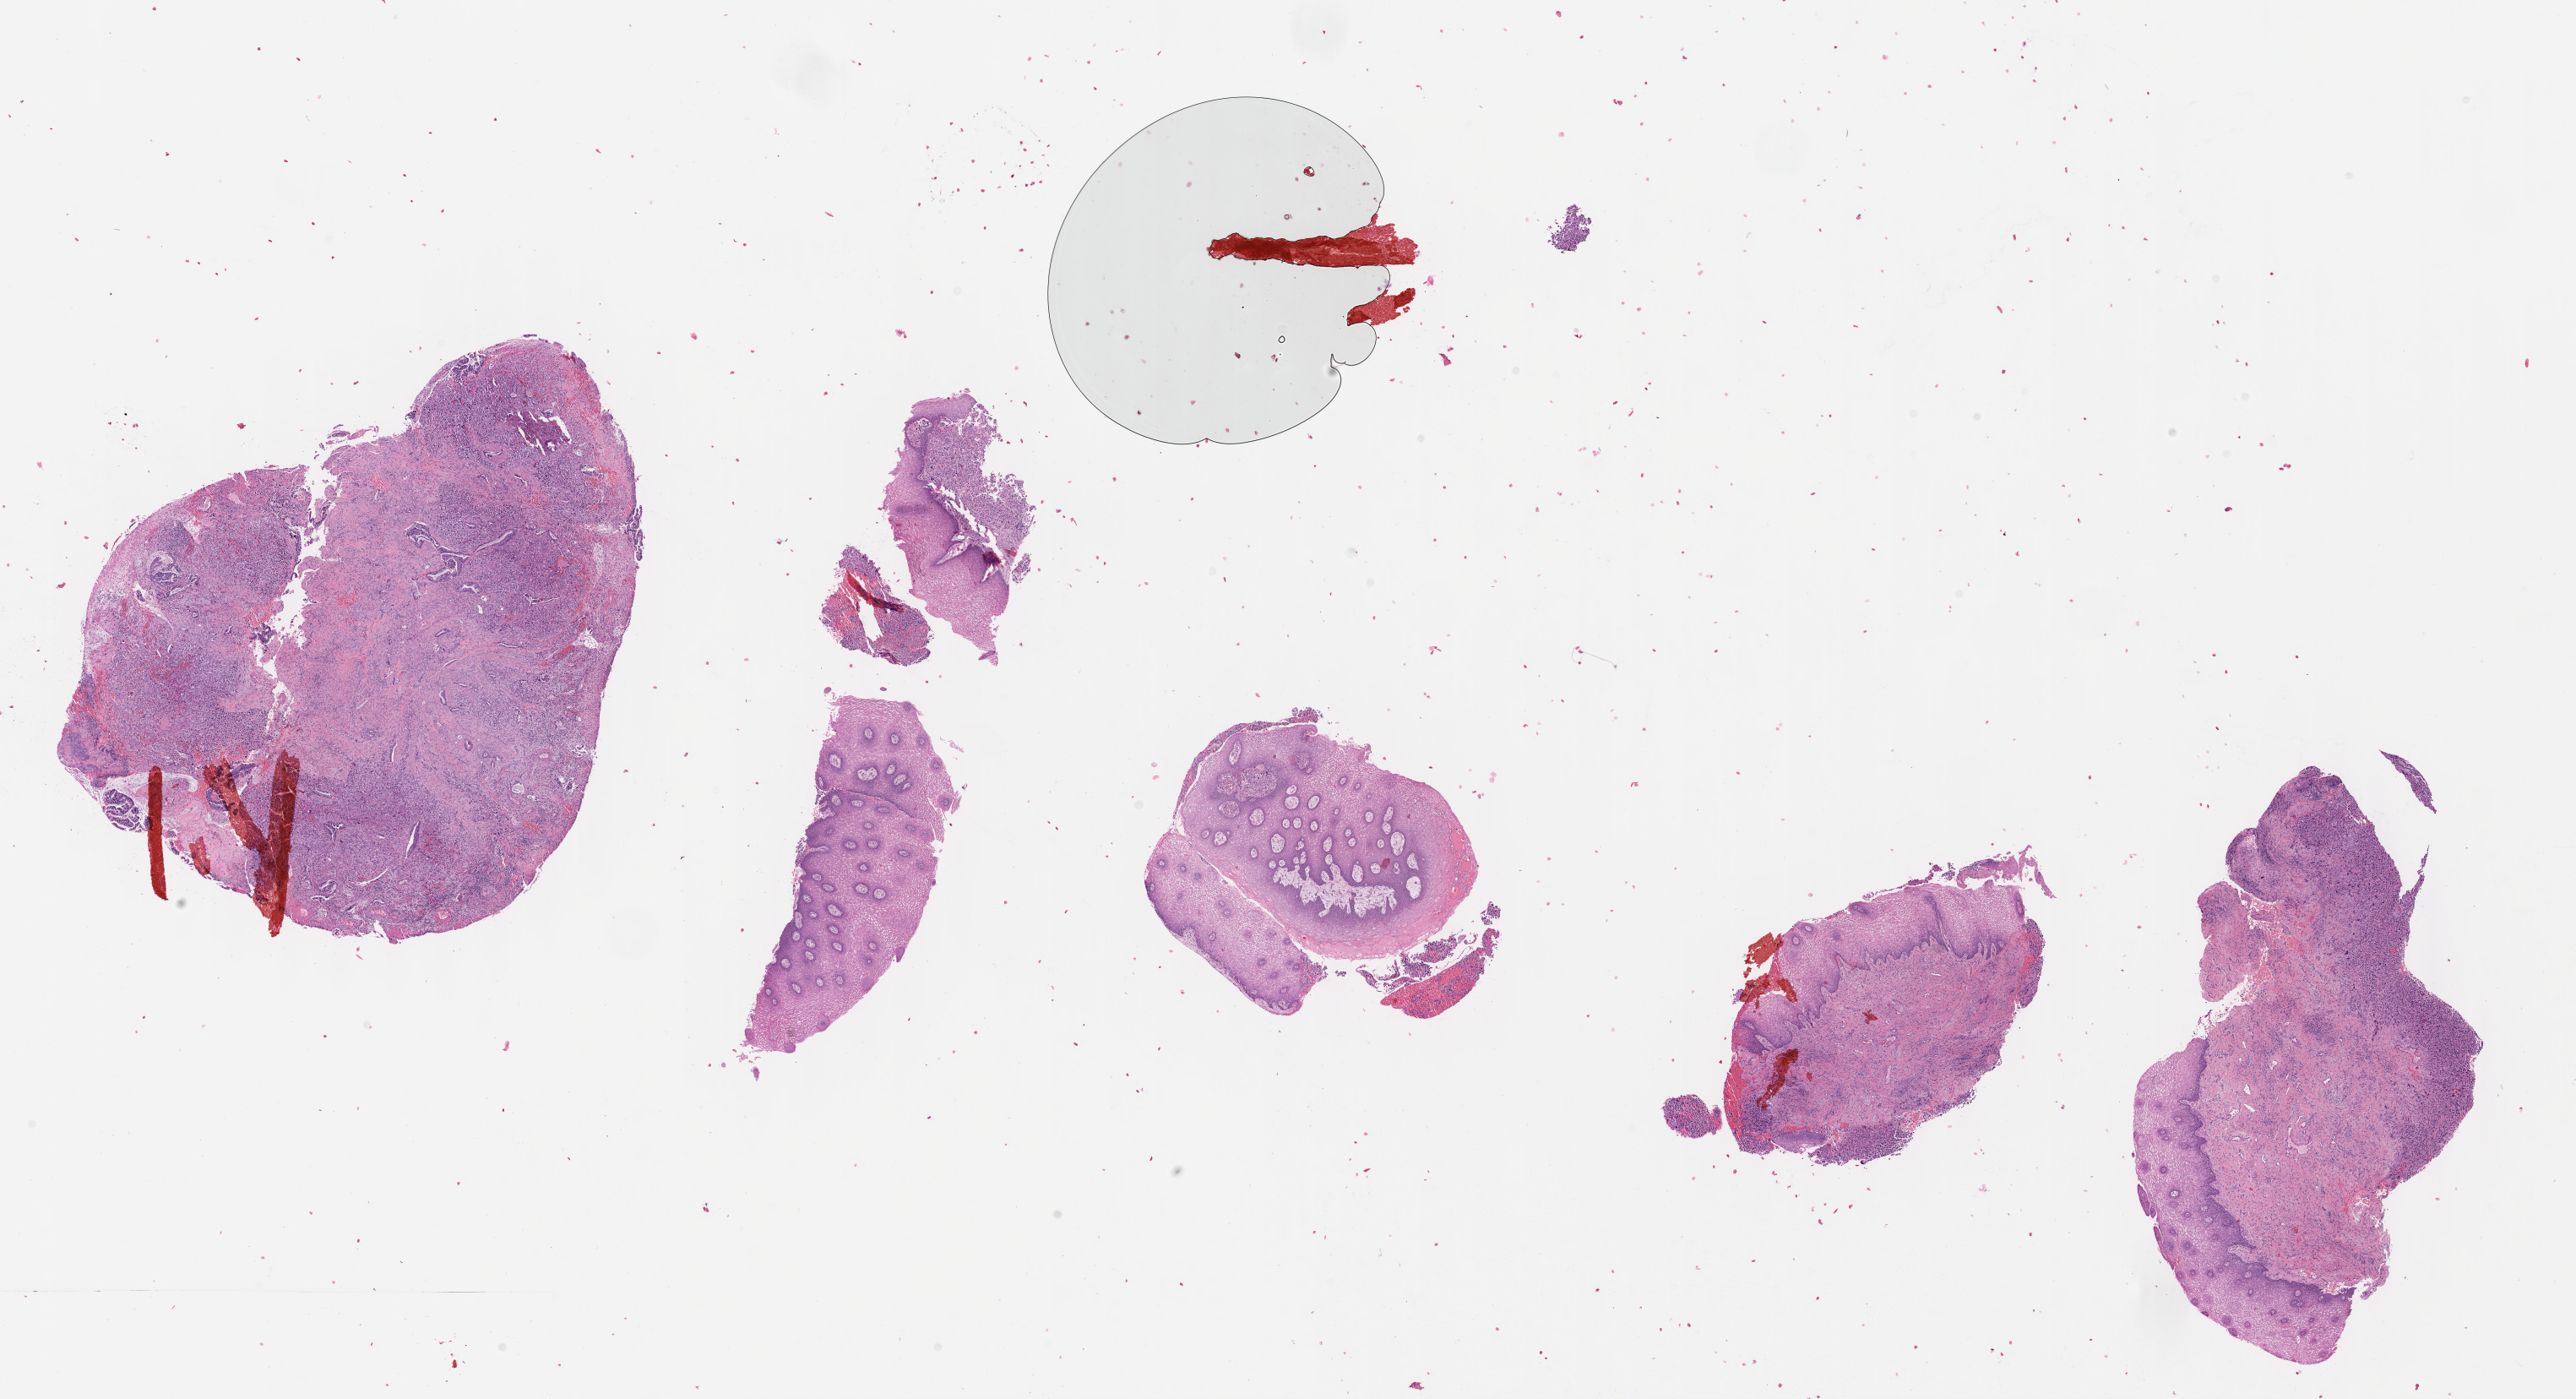
Digitized Hematoxylin and eosin (H&E) stained tissue section (whole slide), a low-resolution overview of the entire scanned area, about 24.6 x 13.4 mm (from a 40x scan). FFPE section. Primary tumour sample from the cervix. Patient: female, age at initial diagnosis 48 years. Histologic grade: G3 (poorly differentiated).
- diagnosis: Squamous cell carcinoma, NOS (cervix uteri)
- FIGO stage: IIIB